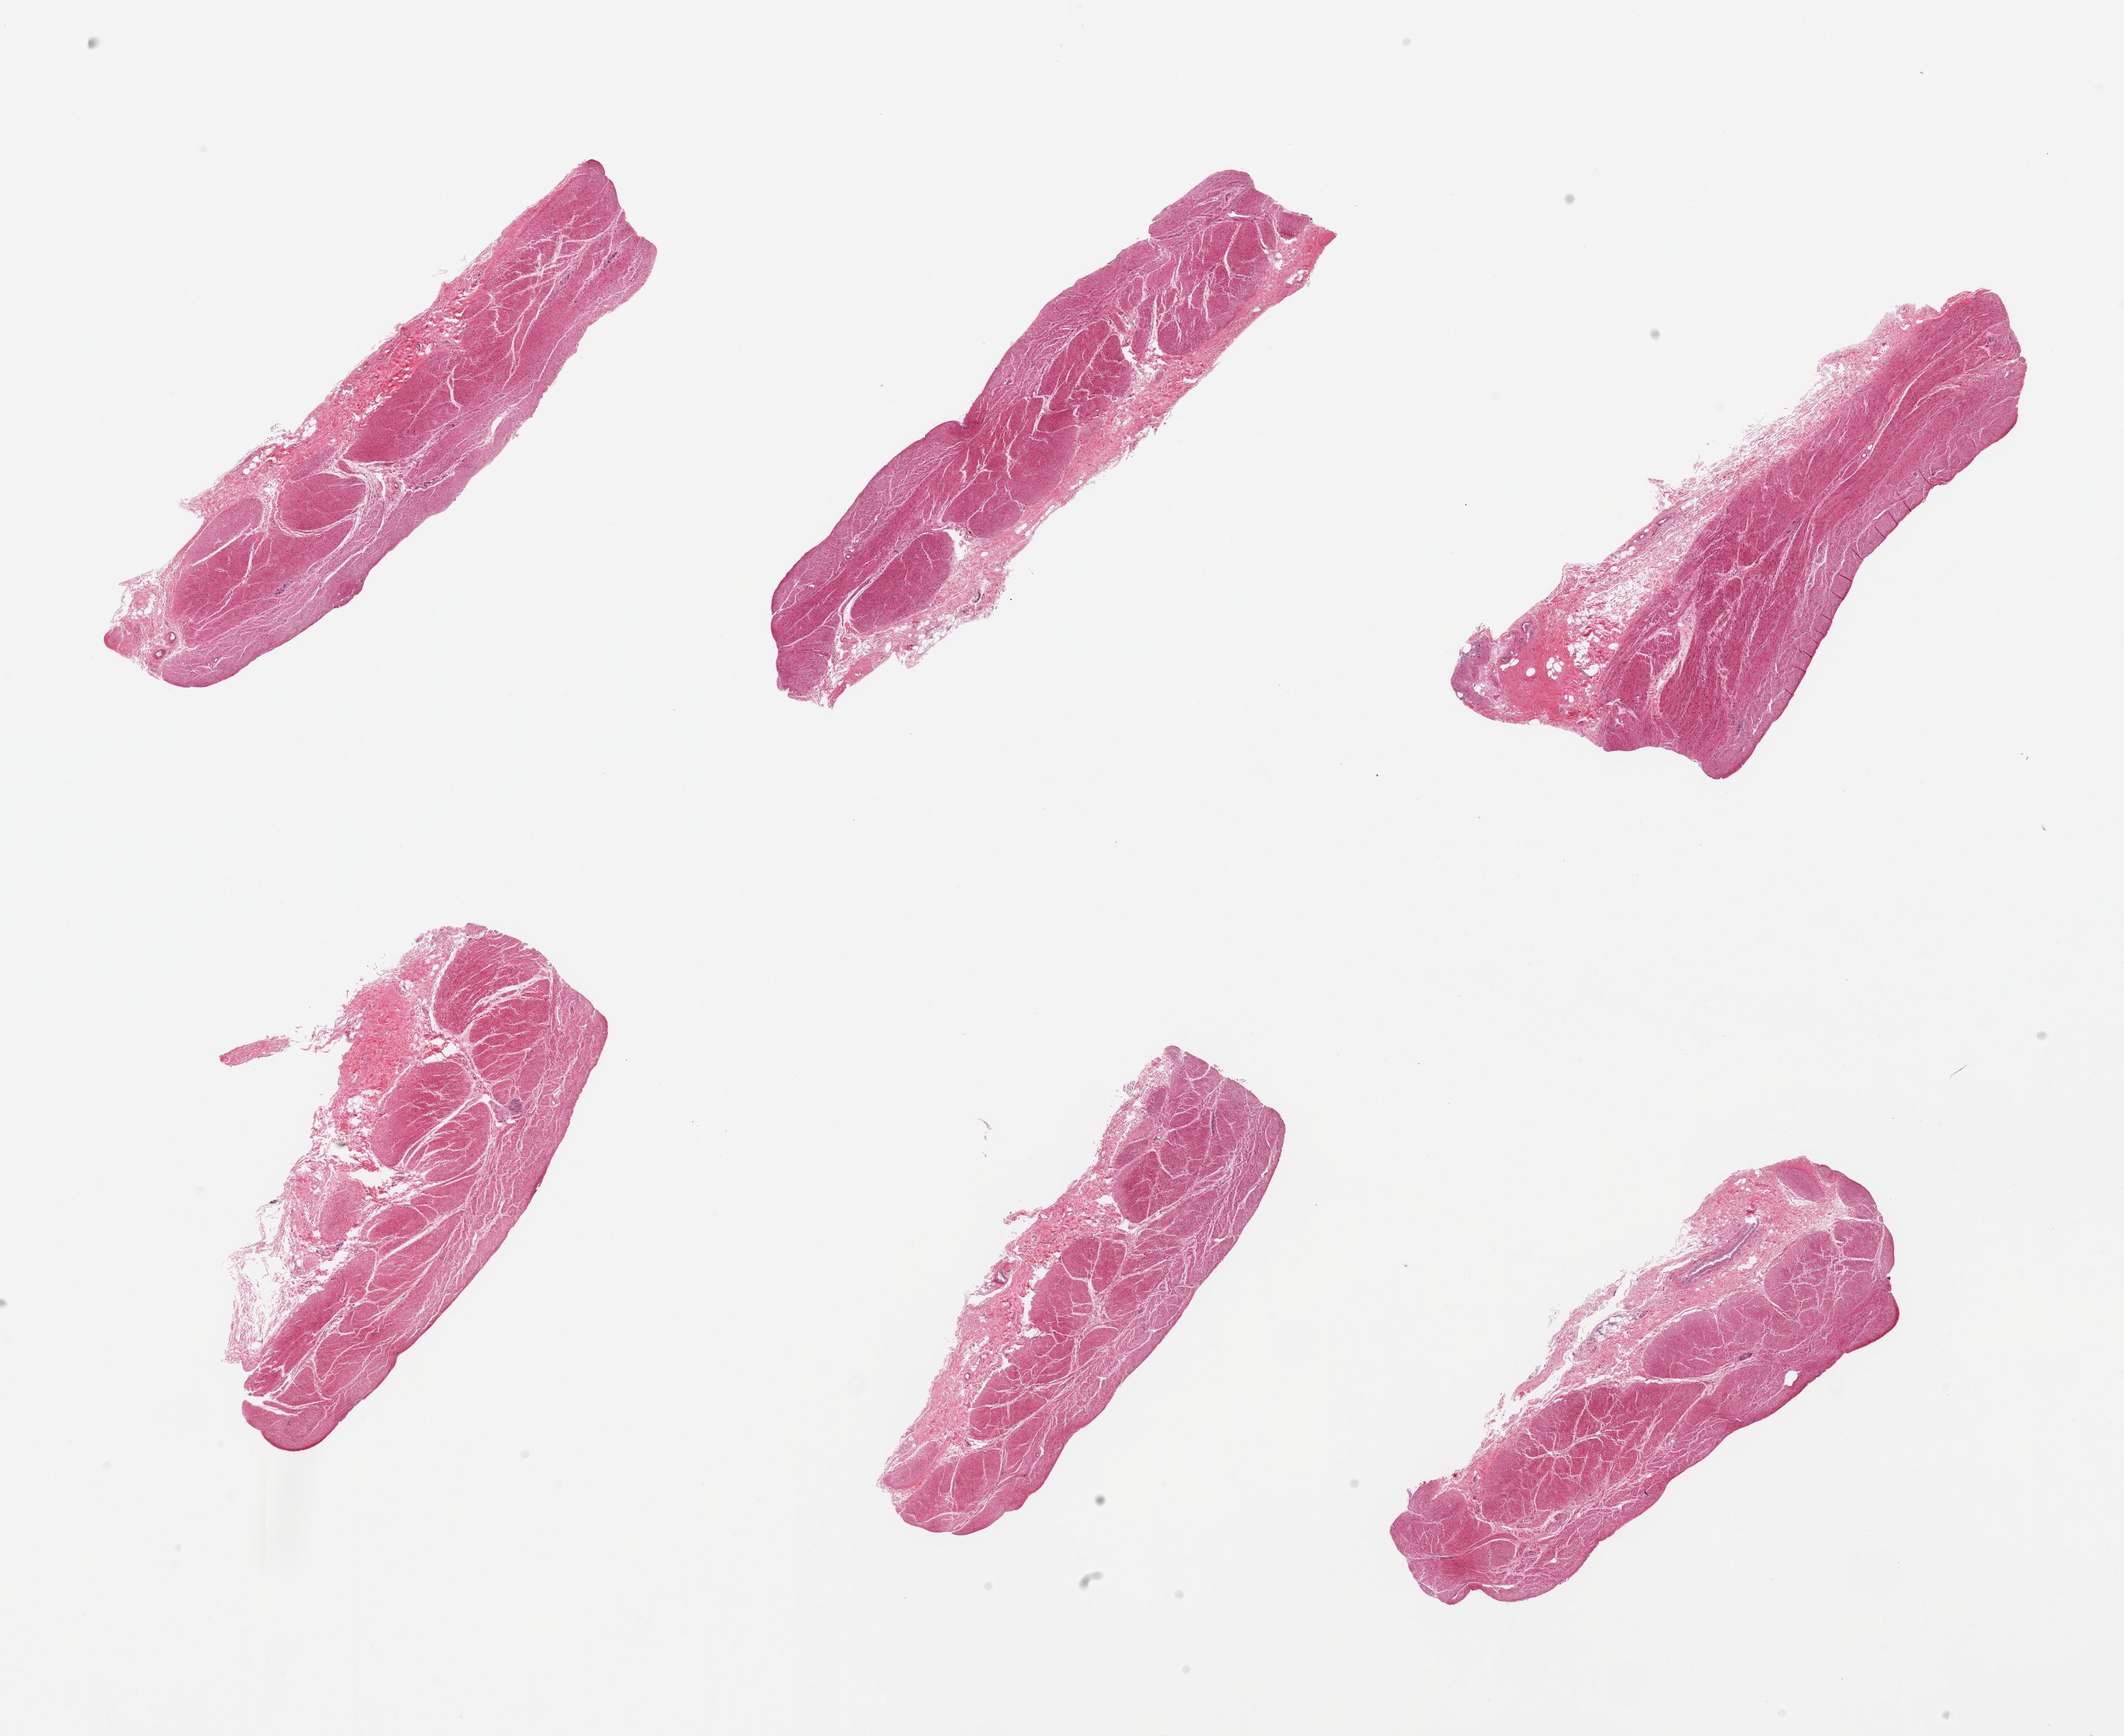
Digitized hematoxylin and eosin (H&E)-stained section, a low-resolution overview of the entire scanned area, about 23.6 x 19.3 mm, PAXgene-fixed paraffin-embedded (PFPE) section, target tissue: stomach, tissue donor sample. Donor sex: female.
- reviewer comment on this tissue sample: 6 pieces, mucosa totally sloughed/denuded